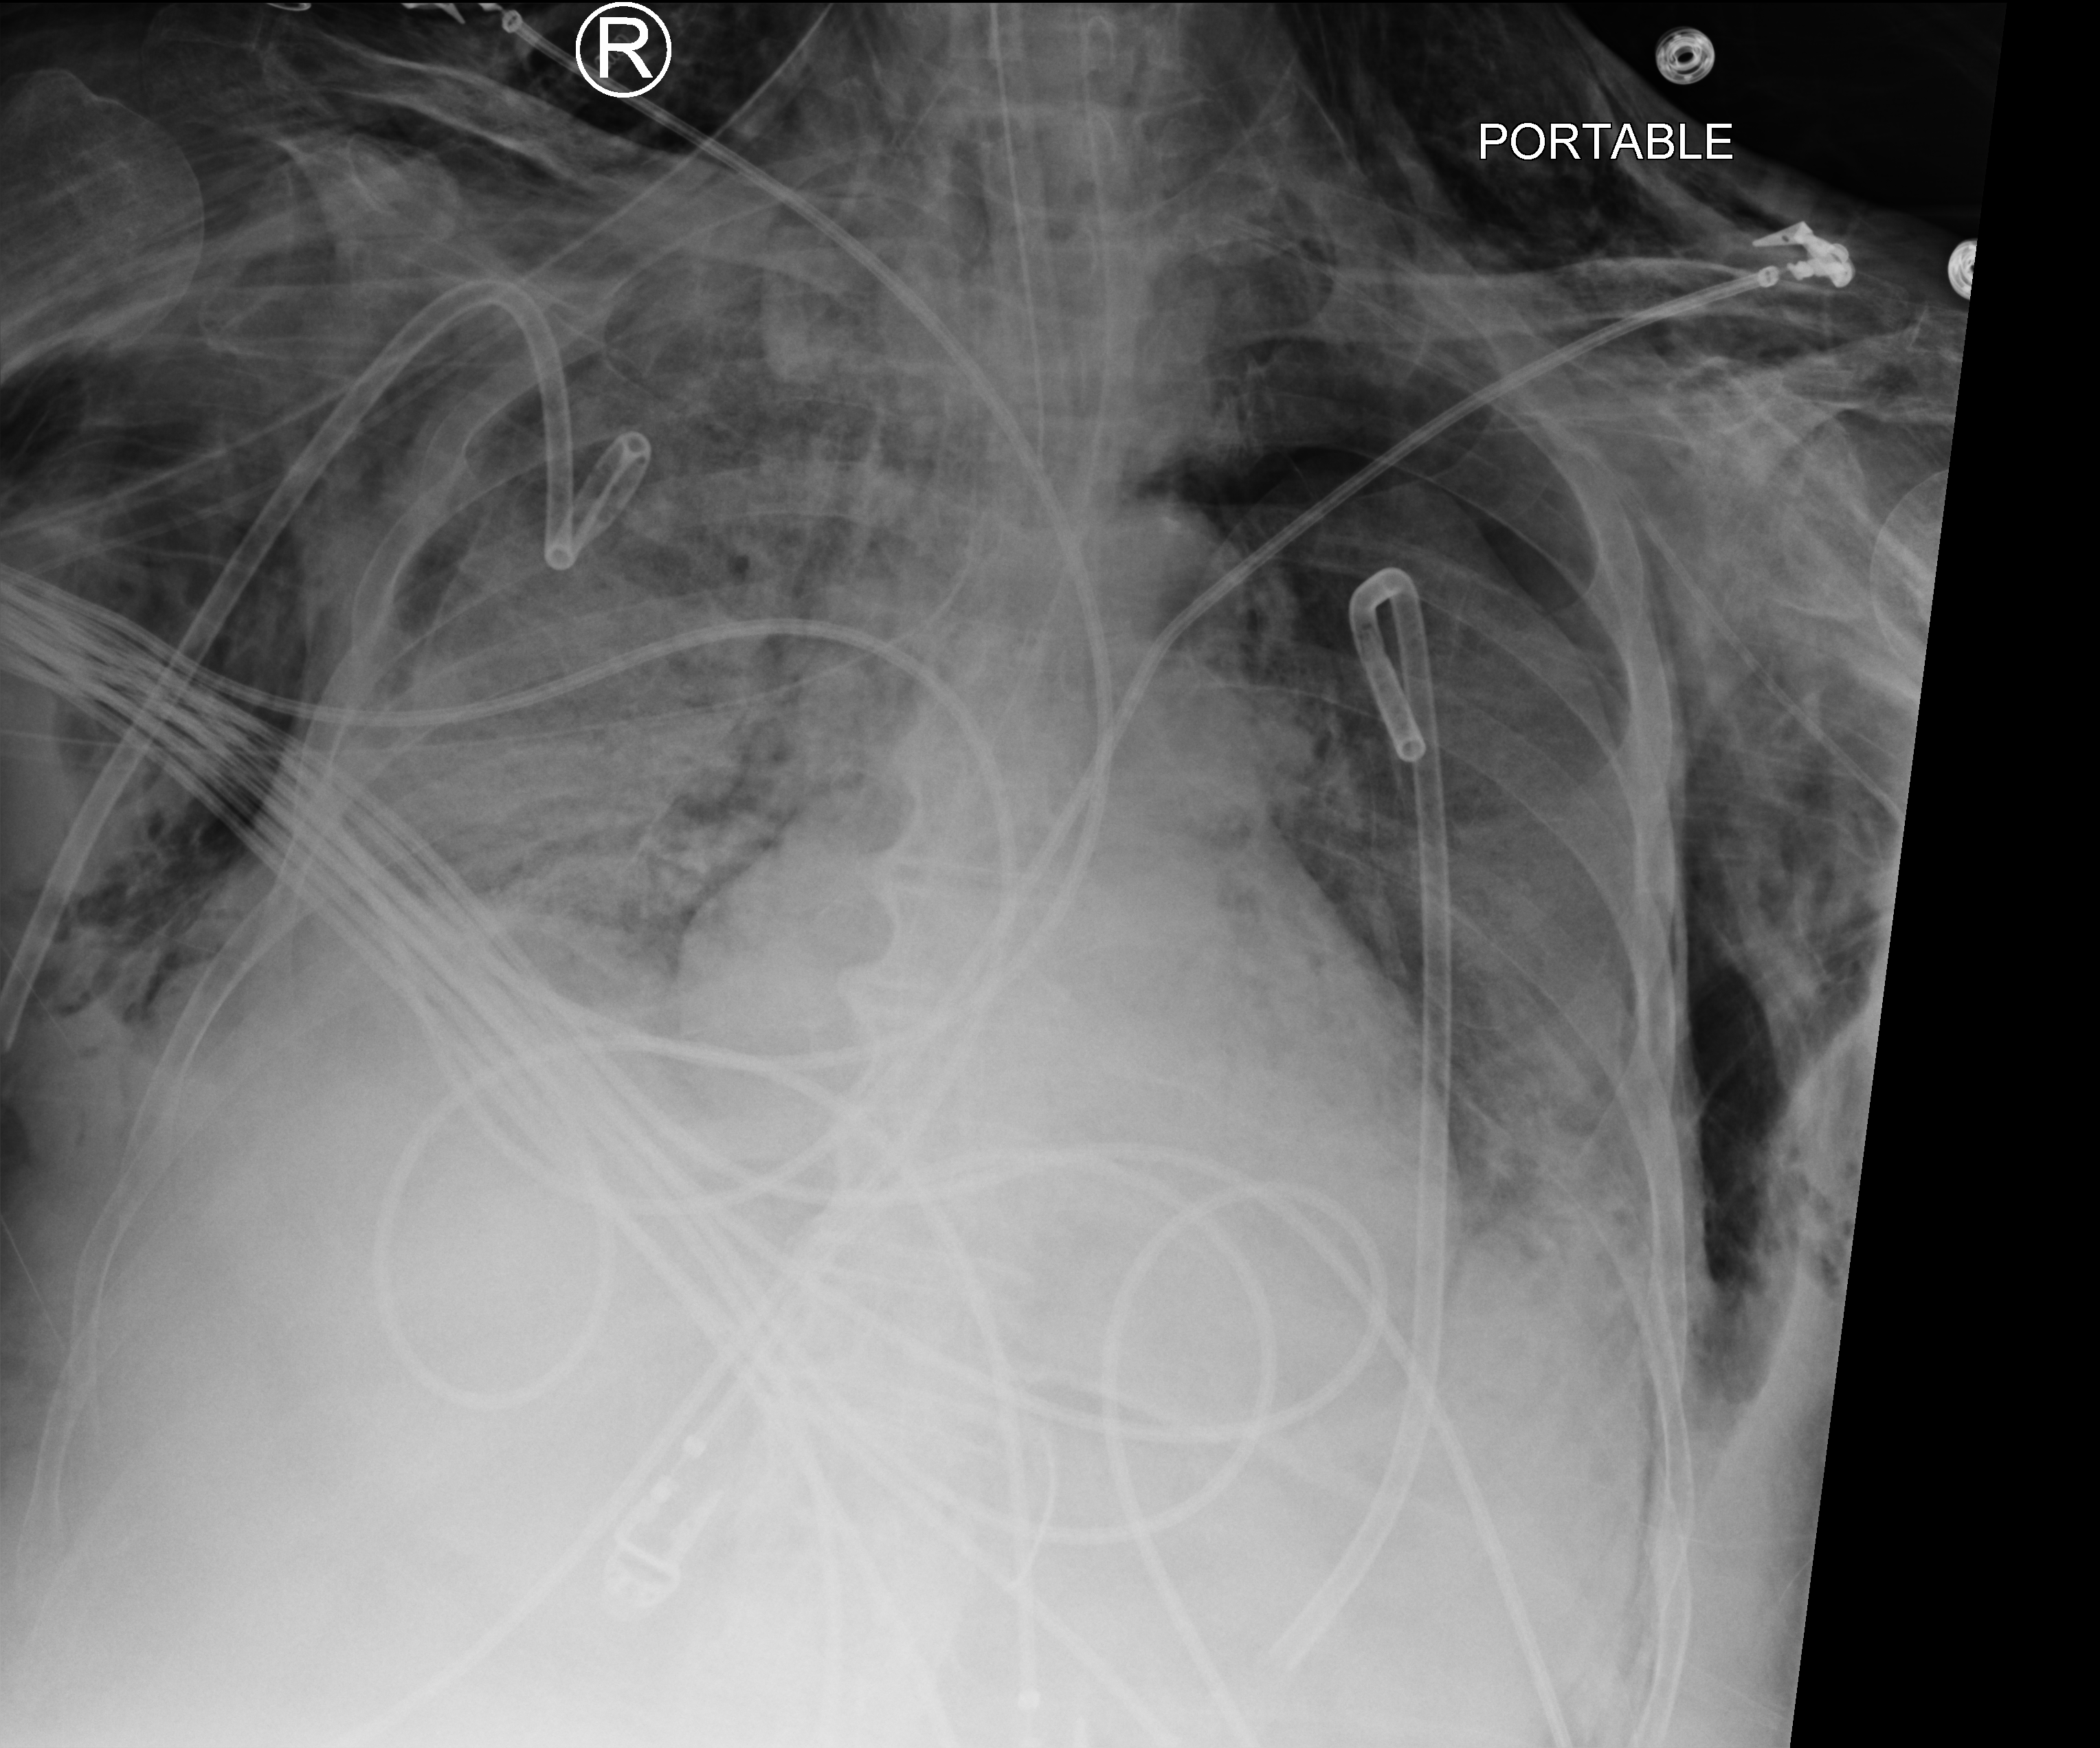
Portable chest radiograph. Male patient hospitalised with COVID-19, age 75–90 years.
Admission-level facts for this patient (not findings on this image; timing relative to this image not recorded):
- mechanically ventilated during this hospital stay: yes
- diabetes (admission record): no
- admitted to intensive care during this hospital stay: yes